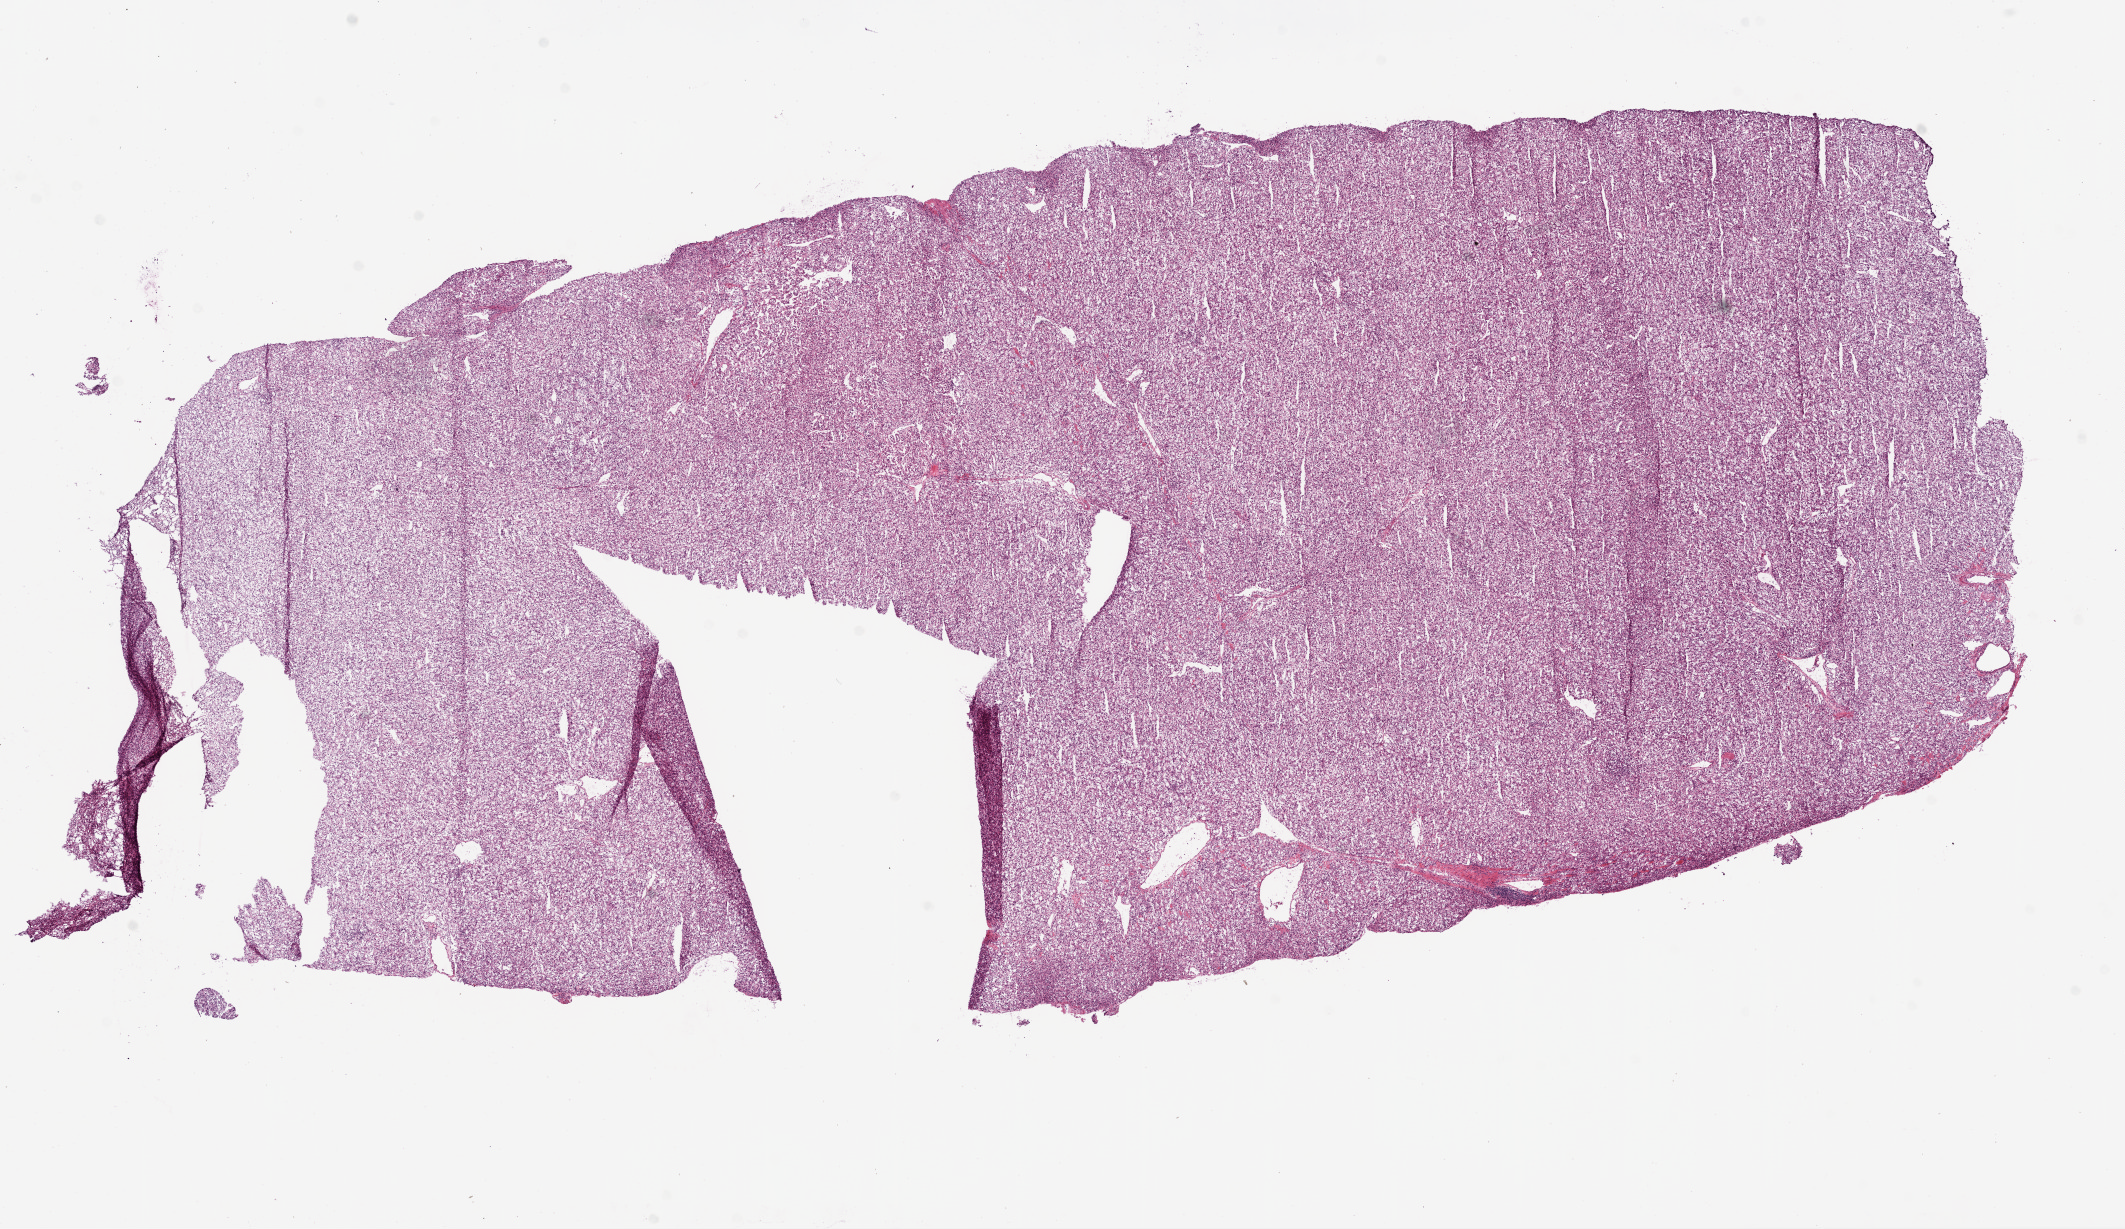
Whole-slide histology image, H&E, a low-resolution overview of the entire scanned area, about 17.1 x 9.9 mm (from a 20x scan). Frozen section from the bottom of the tissue portion. Sample: primary tumour, kidney. Male, age 52 years at initial diagnosis. Histologic grade: G2 (moderately differentiated). Slide review estimates, as recorded: tumour cells 95%, tumour nuclei 90%, normal cells 0%, stromal cells 5%, necrosis 0%.
TNM: T3a N0 M1. AJCC pathologic stage: IV. Pathologic diagnosis: Clear cell adenocarcinoma, NOS.